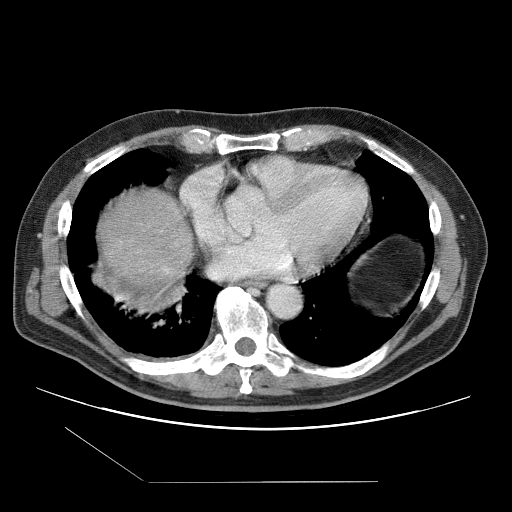
Contrast-enhanced abdominal CT (liver protocol), one axial slice; slice 100 of 109 in the series (ordered by position); 120 kVp; one of 2 acquisitions stored at this slice position; soft-tissue window (W 400 / L 40 HU); 512 × 512 image matrix. Case-level facts recorded for this patient, not image findings: diagnosis: hepatocellular carcinoma (patient treated with transarterial chemoembolisation; whether this scan precedes or follows treatment is not stated here); TNM stage (as recorded): Stage-IIIB.
Outlined on this slice (semi-automatically segmented with operator editing):
- liver parenchyma outside the tumour (the mass and vessels are separate outlines, so this box may not span the whole liver): box from (x=100, y=190) to (x=192, y=284) px
- liver vessels: (x=165, y=269)–(x=168, y=272)